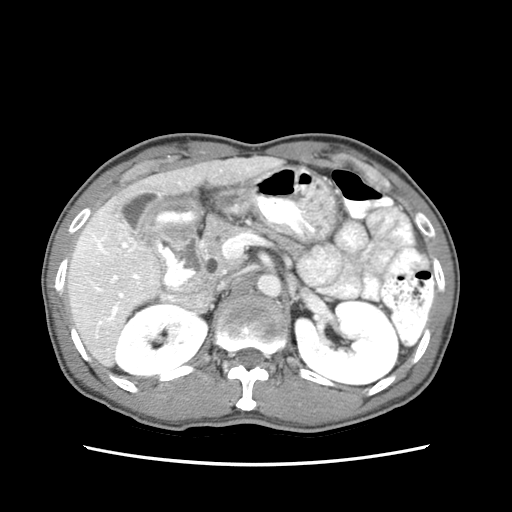
Contrast-enhanced abdominal CT (liver protocol), one axial slice. Slice 32 of 79 in the series (ordered by position). Reconstruction kernel STANDARD. Soft-tissue window (W 400 / L 40 HU). 2.5 mm slice thickness. 512 × 512 image matrix, field of view 320 × 320 mm. Case-level facts recorded for this patient, not image findings: diagnosis: hepatocellular carcinoma (patient treated with transarterial chemoembolisation; whether this scan precedes or follows treatment is not stated here); TNM stage (as recorded): Stage-IIIB; Child-Pugh class: A; tumour differentiation: moderately differentiated; tumour nodularity: multinodular.
Structures marked on this image (semi-automatically segmented with operator editing):
- liver parenchyma outside the tumour (the mass and vessels are separate outlines, so this box may not span the whole liver): bounding box (x1, y1, x2, y2) in pixels: (66, 154, 284, 364)
- liver vessels: (78, 162, 257, 341)